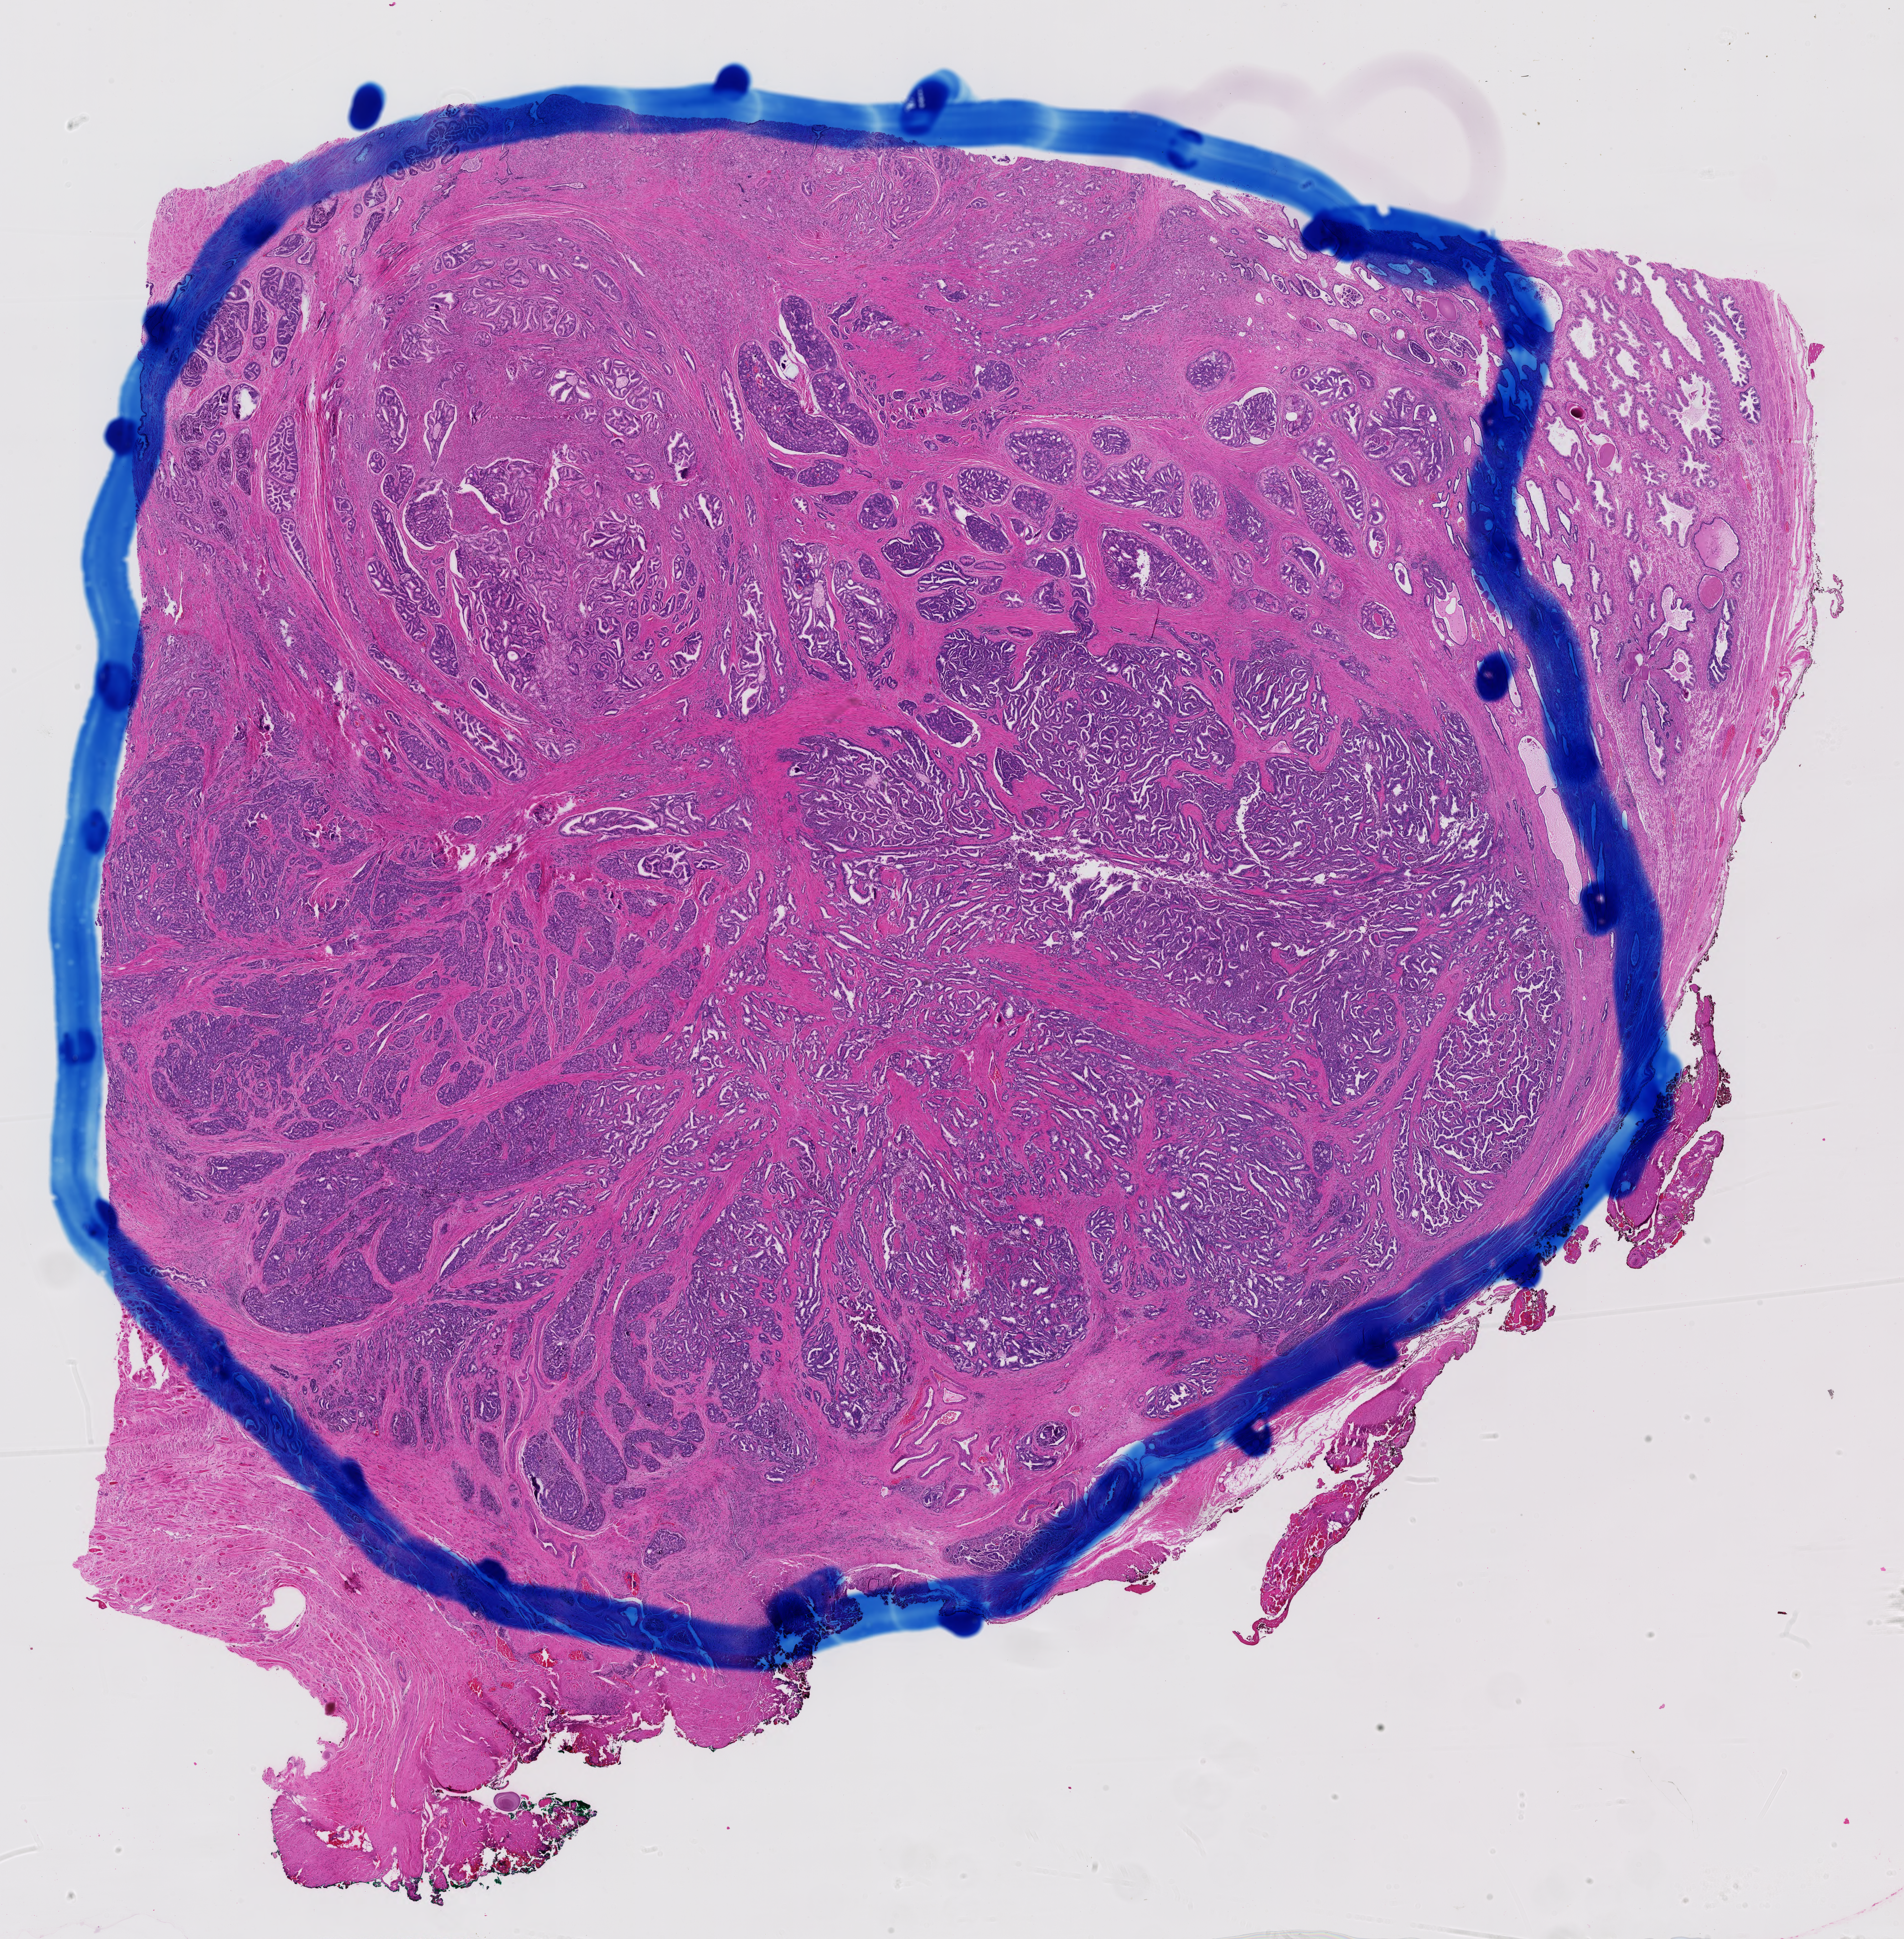
Whole-slide histology image, Hematoxylin and eosin (H&E) stained — whole scanned area (about 22.3 x 22.7 mm, slide scanned at 40x) shown as a low-resolution overview; formalin-fixed paraffin-embedded (FFPE) diagnostic section; sample: primary tumour, prostate. Patient: male, age at initial diagnosis 63 years. Gleason score: 9 (4+5).
Lymph nodes positive (case pathology): 1 of 15 examined. Pathologic diagnosis: Adenocarcinoma, NOS (prostate gland).